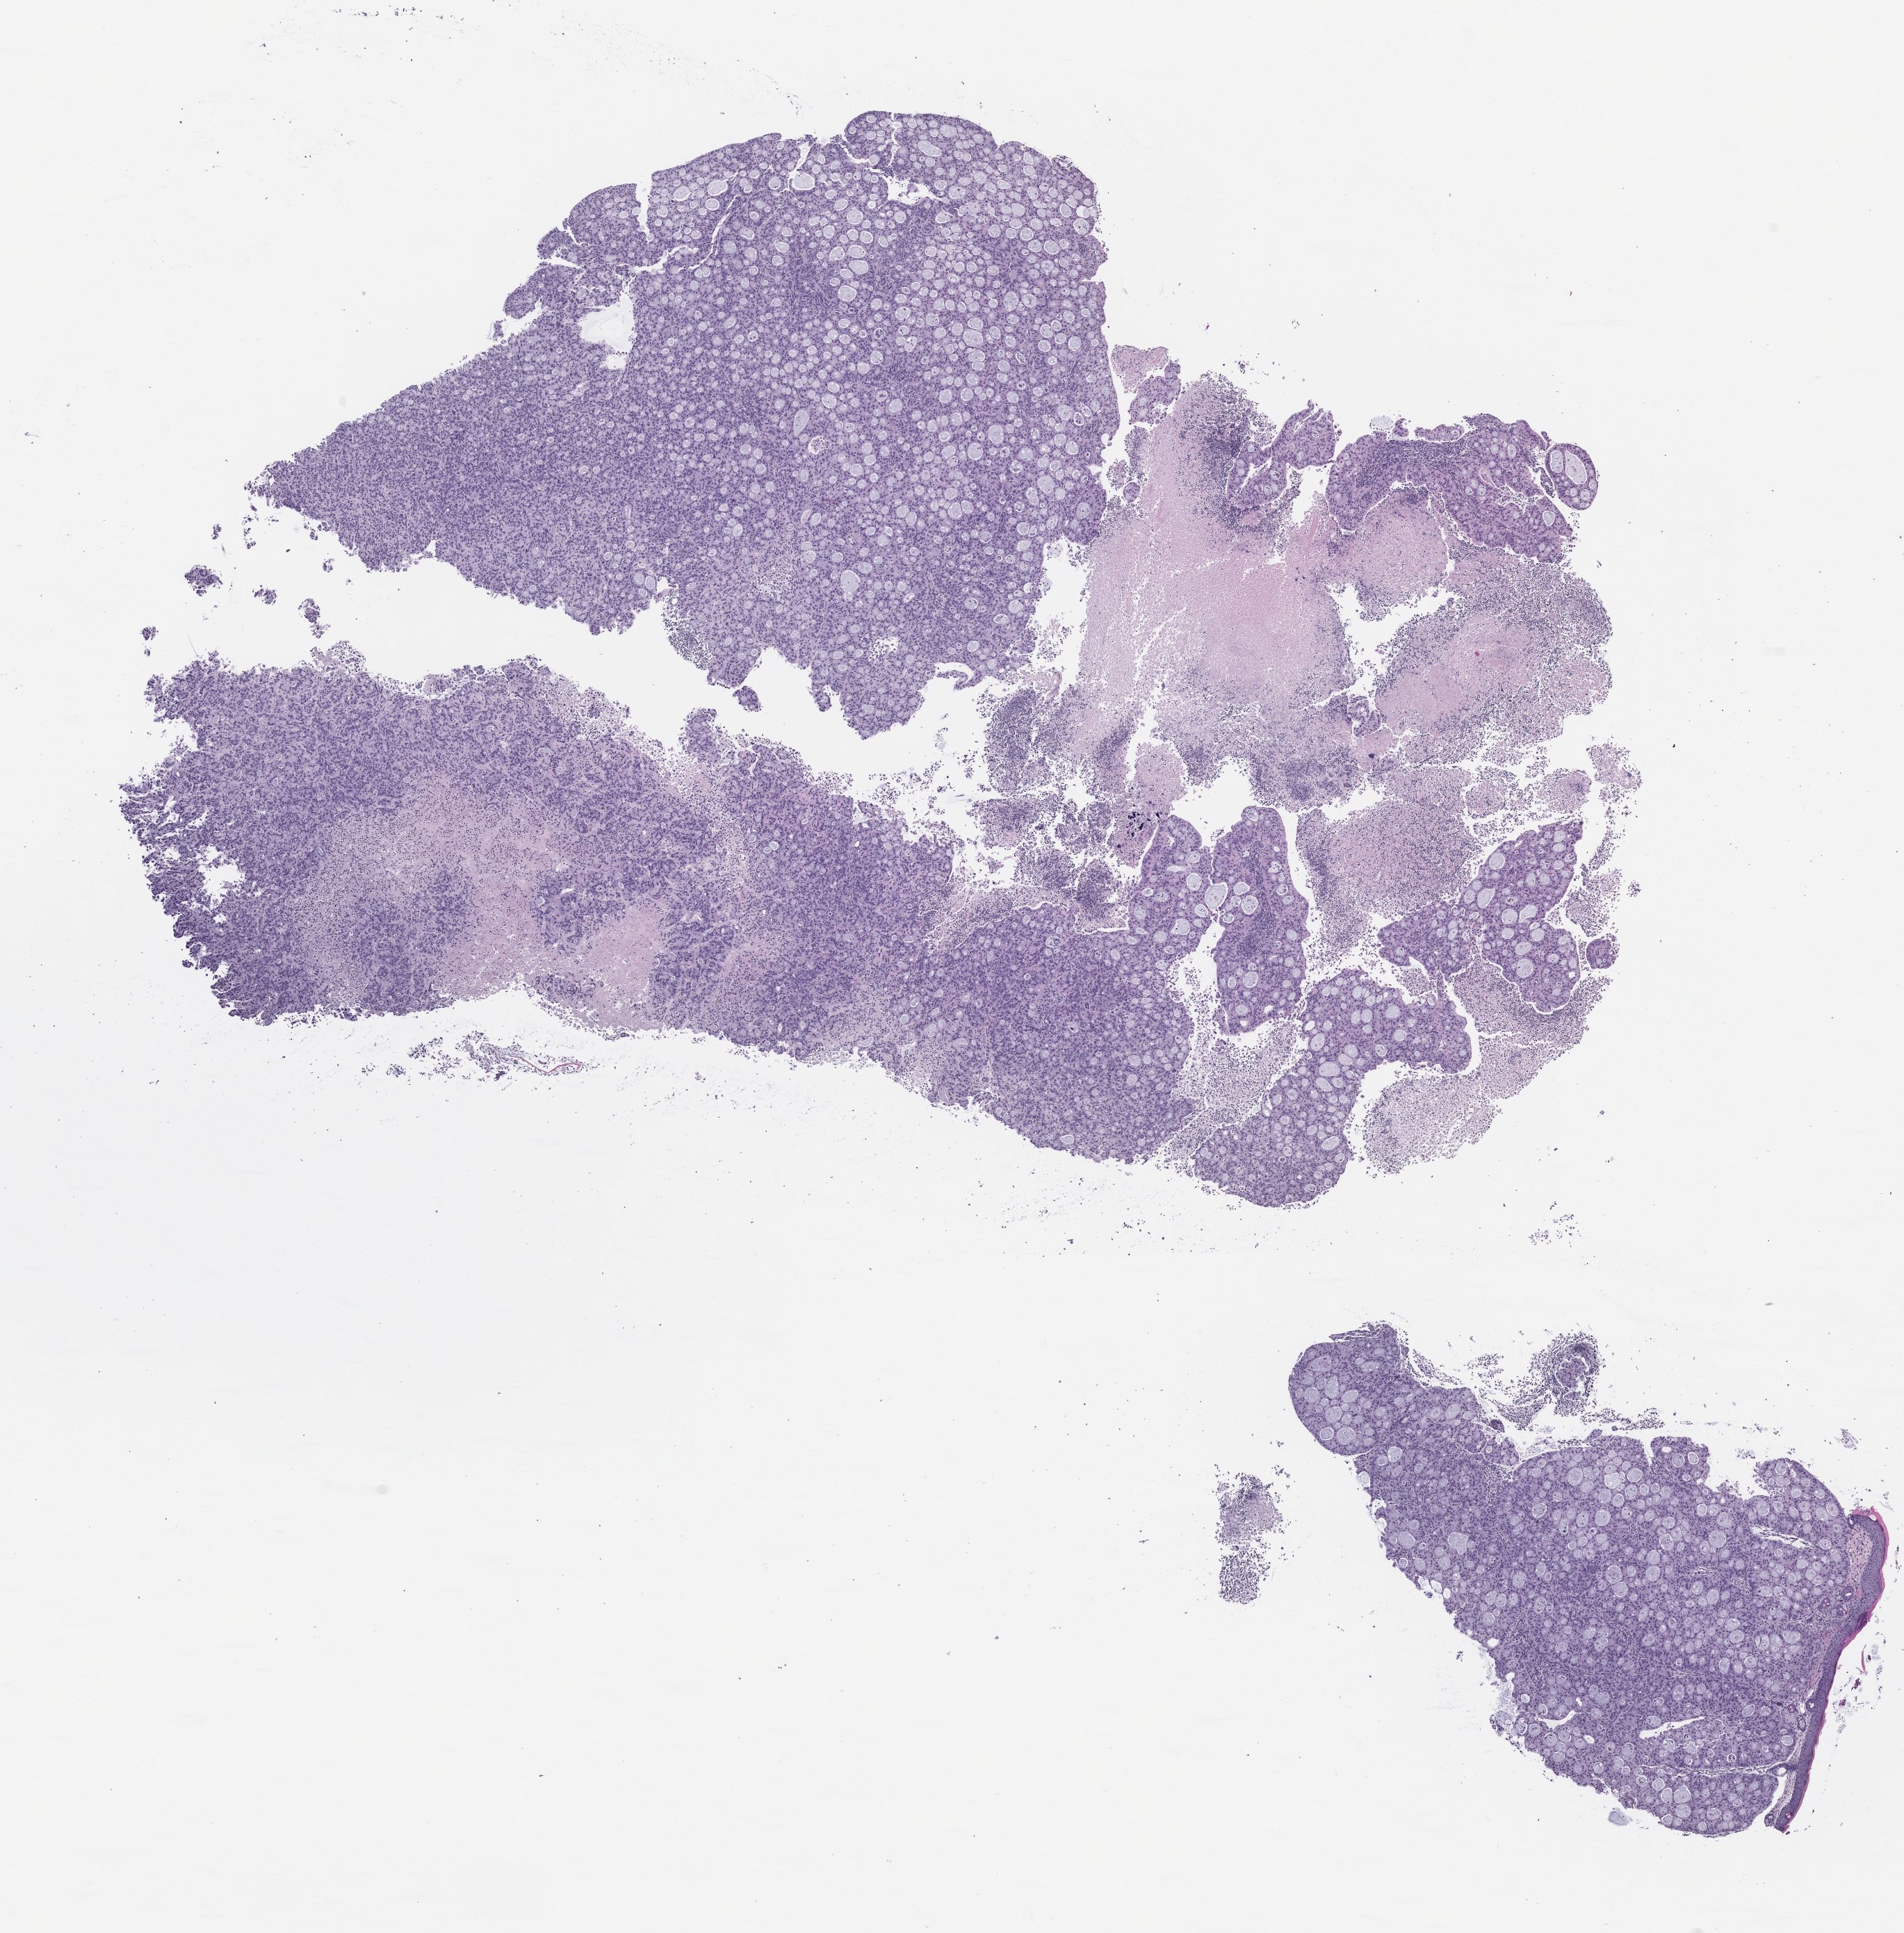
Whole-slide image, haematoxylin and eosin: patient-derived xenograft (human tumor grown in a mouse) — low-resolution overview of the scanned area, about 11.0 x 11.2 mm; formalin-fixed, paraffin-embedded (FFPE) tissue; originating tumor site category: pancreas.
- originating patient diagnosis: Pancreatic Adenocarcinoma